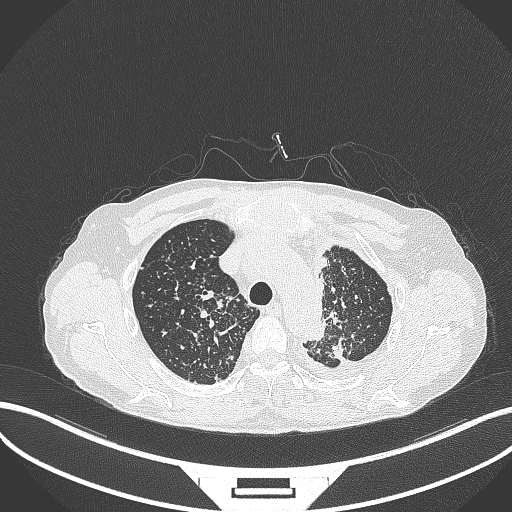
Chest CT, one axial slice; position 276 of 325 along the scan axis; reconstruction kernel B70f; lung window (W 1500 / L -600 HU); 1 mm slice thickness; 512 × 512 image matrix, field of view 400 × 400 mm. Male patient, age 58 years. From the clinical record (not read from this slice): clinical TNM (as recorded): T1c N3 M1.
Outlined on this slice (bounding box drawn by a radiologist):
- lung tumour (recorded histology: adenocarcinoma): bounding box [x1, y1, x2, y2] px = [330, 337, 347, 361]